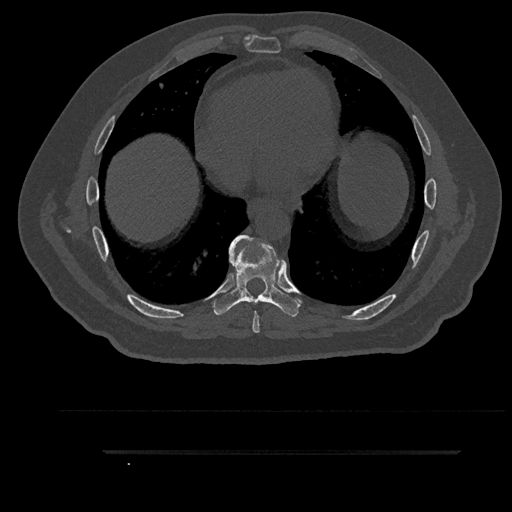
CT including the spine, one axial slice. Position 491 of 797 along the scan axis. Reconstruction kernel Br40s/3. 120 kVp. Bone window (W 1800 / L 400 HU). 0.5 mm slice thickness. 512 × 512 image matrix, field of view 432 × 432 mm. Patient: male, 63 years. From the clinical record (not read from this slice): primary cancer: renal; vertebrae with lytic lesions (as recorded): T8.
Structures marked on this image (semi-automatic segmentation, software-assisted and operator-edited):
- T7 vertebra: bounding box [x1, y1, x2, y2] px = [240, 237, 260, 333]
- T8 vertebra: [212, 235, 301, 317]